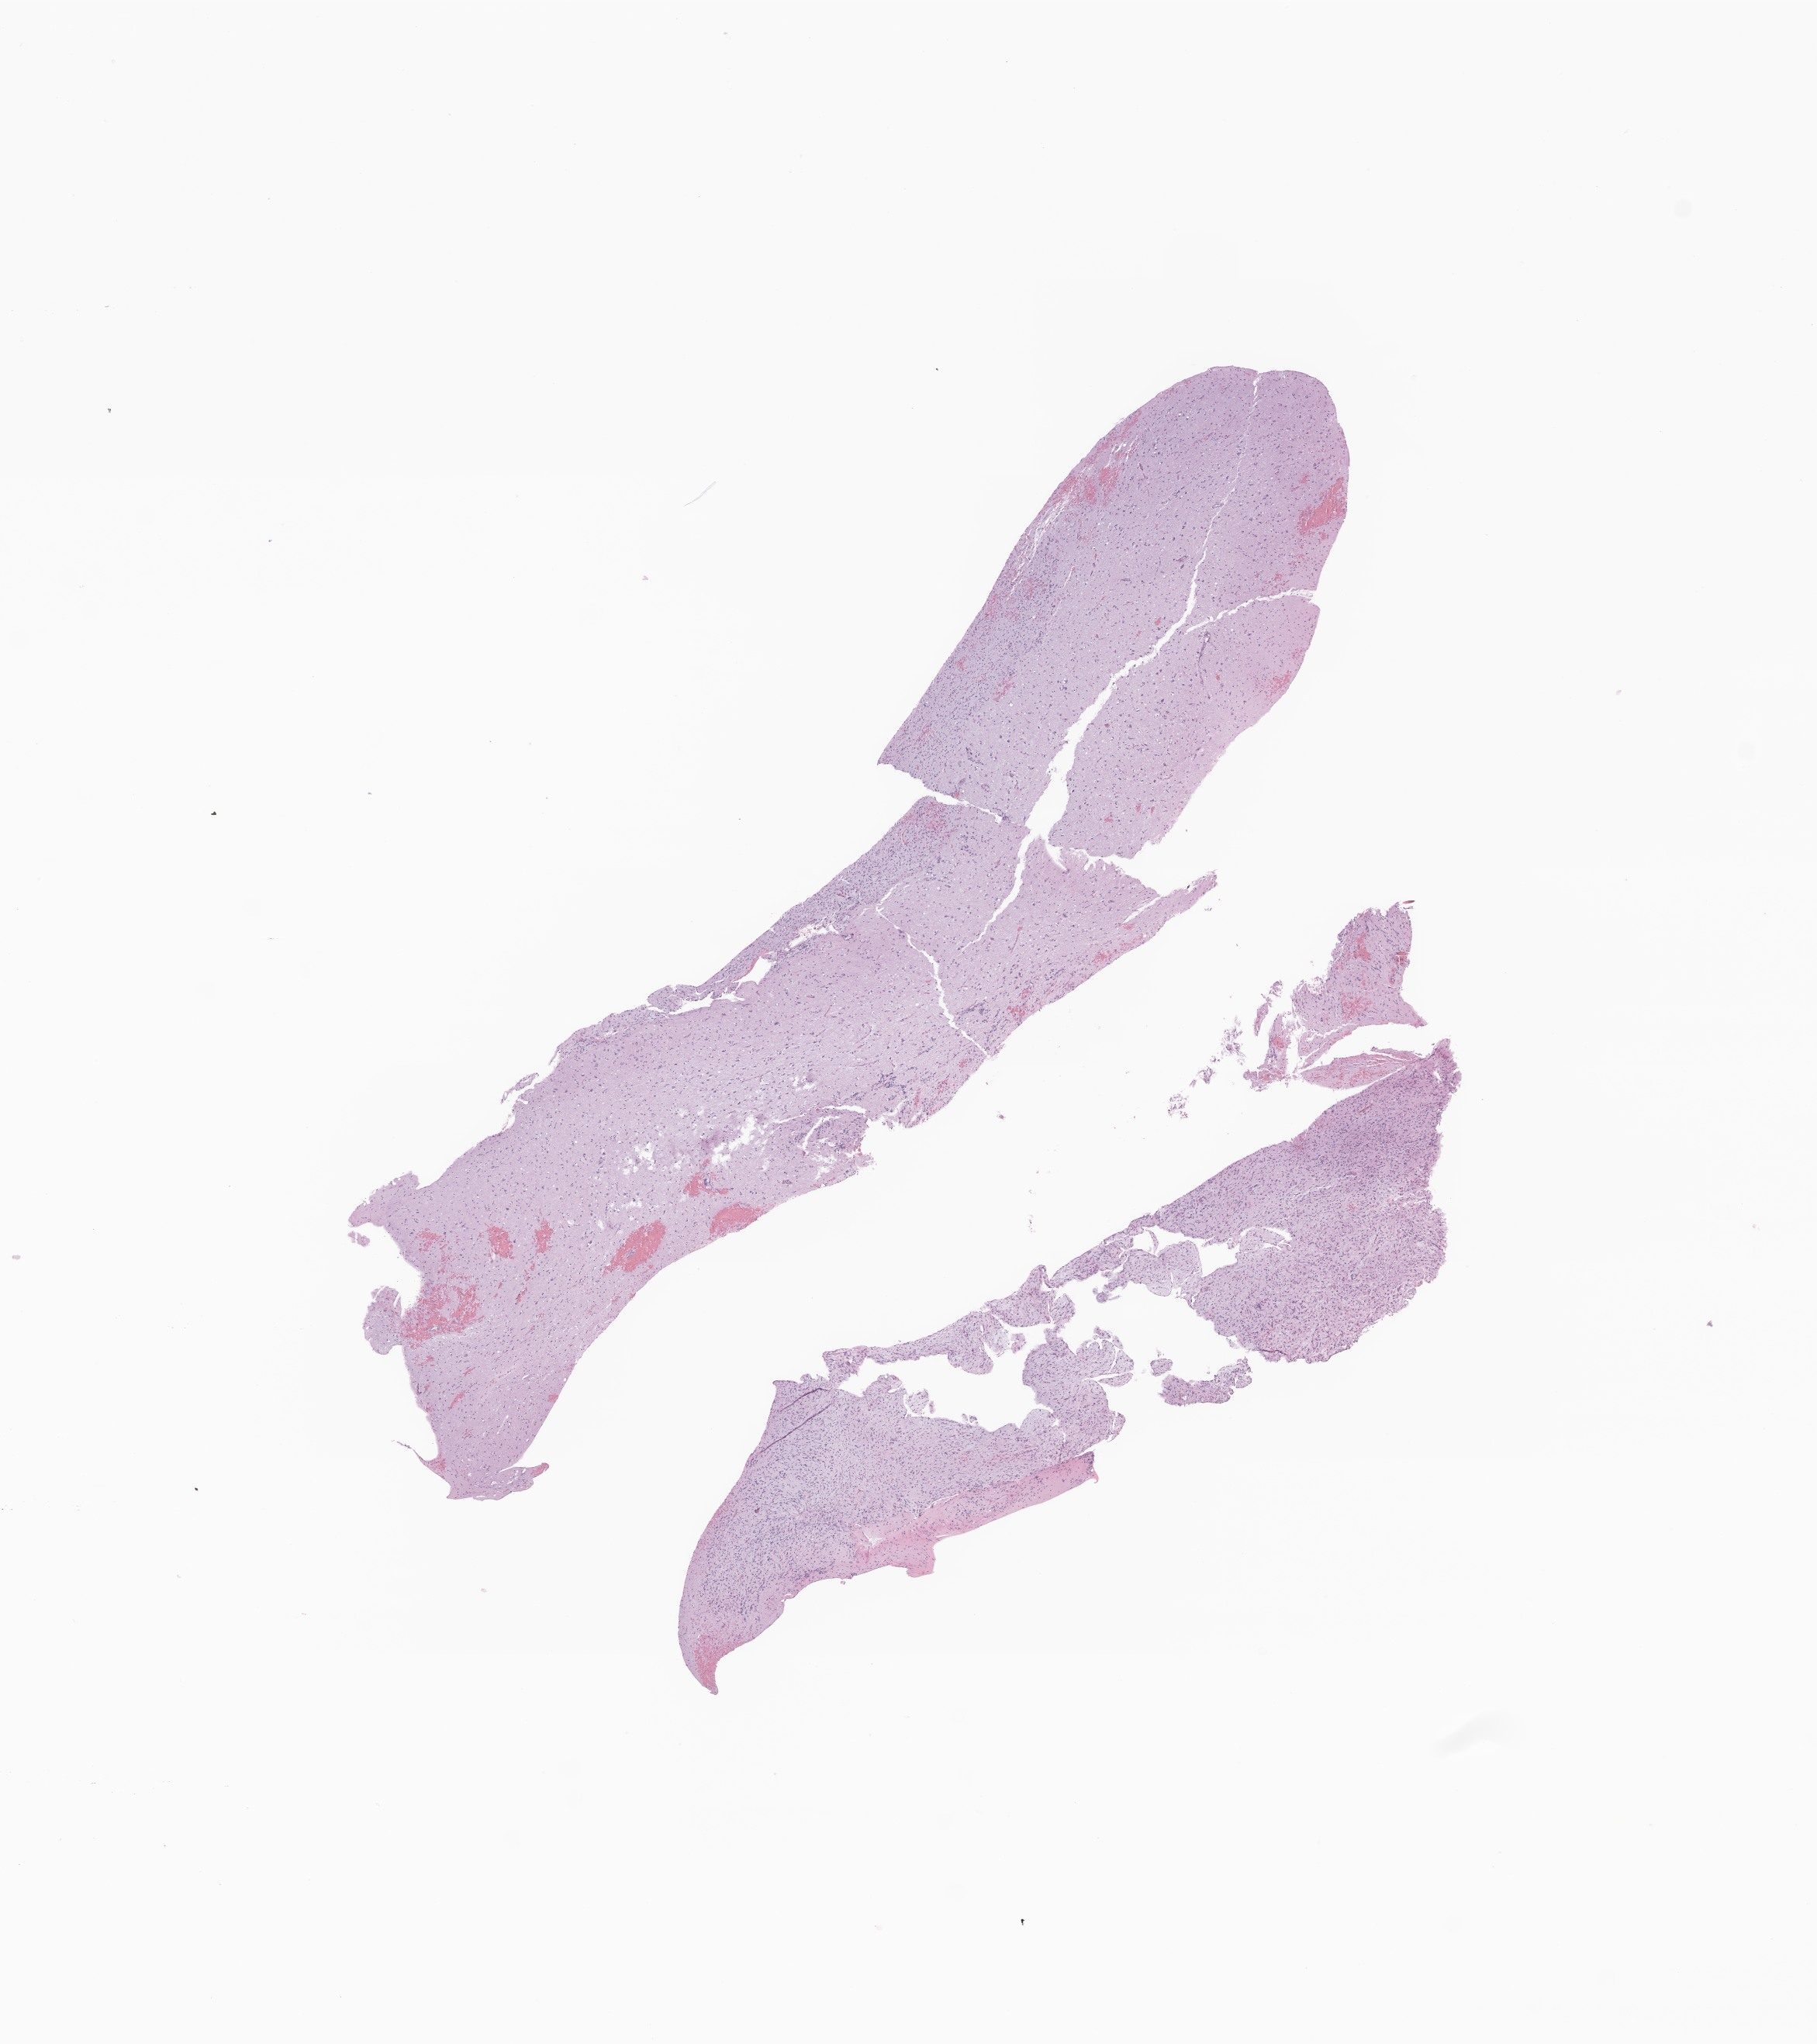
Digitized H&E-stained section of tumor tissue from the brain — a low-resolution overview of the entire scanned area, about 9.9 x 11.1 mm, formalin-fixed paraffin-embedded section. Patient: female, age 83 months.
Recorded diagnosis: Pilocytic astrocytoma.